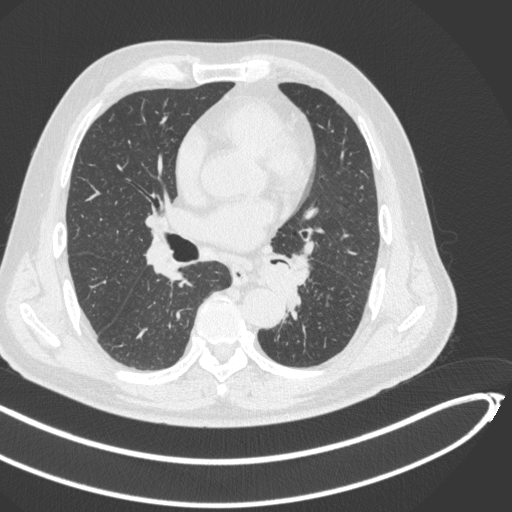
Chest CT, one axial slice; position 245 of 466 along the scan axis; reconstruction kernel B31f; 120 kVp; lung window (W 1500 / L -600 HU); 1 mm slice thickness; 512 × 512 image matrix, field of view 400 × 400 mm. Male patient, age 64 years. From the clinical record (not read from this slice): clinical TNM (as recorded): T1c N0 M0.
Outlined on this slice (rectangle marked by the reading radiologist):
- lung tumour (recorded histology: squamous cell carcinoma): box from (x=255, y=254) to (x=305, y=309) px